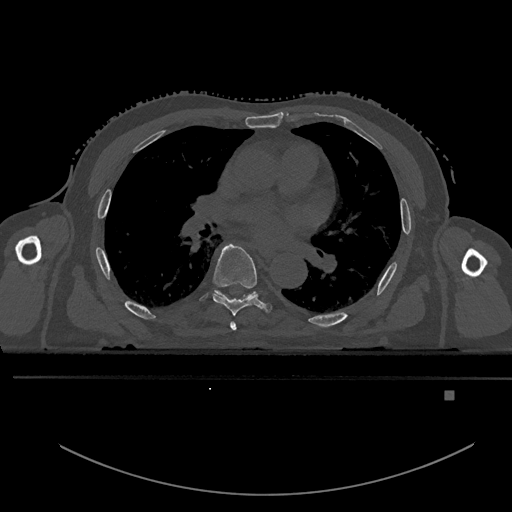
CT including the spine, one axial slice; position 302 of 969 along the scan axis; bone window (W 1800 / L 400 HU); 512 × 512 image matrix. Male patient, age 82 years. Case-level facts recorded for this patient, not image findings: primary cancer: prostate; vertebrae with lytic lesions (as recorded): T11, T9, T8, T2.
Outlined on this slice (semi-automatic segmentation, software-assisted and operator-edited):
- T5 vertebra: bounding box (x1, y1, x2, y2) in pixels: (230, 322, 237, 331)
- T6 vertebra: (212, 244, 273, 316)
- T7 vertebra: (249, 293, 254, 297)